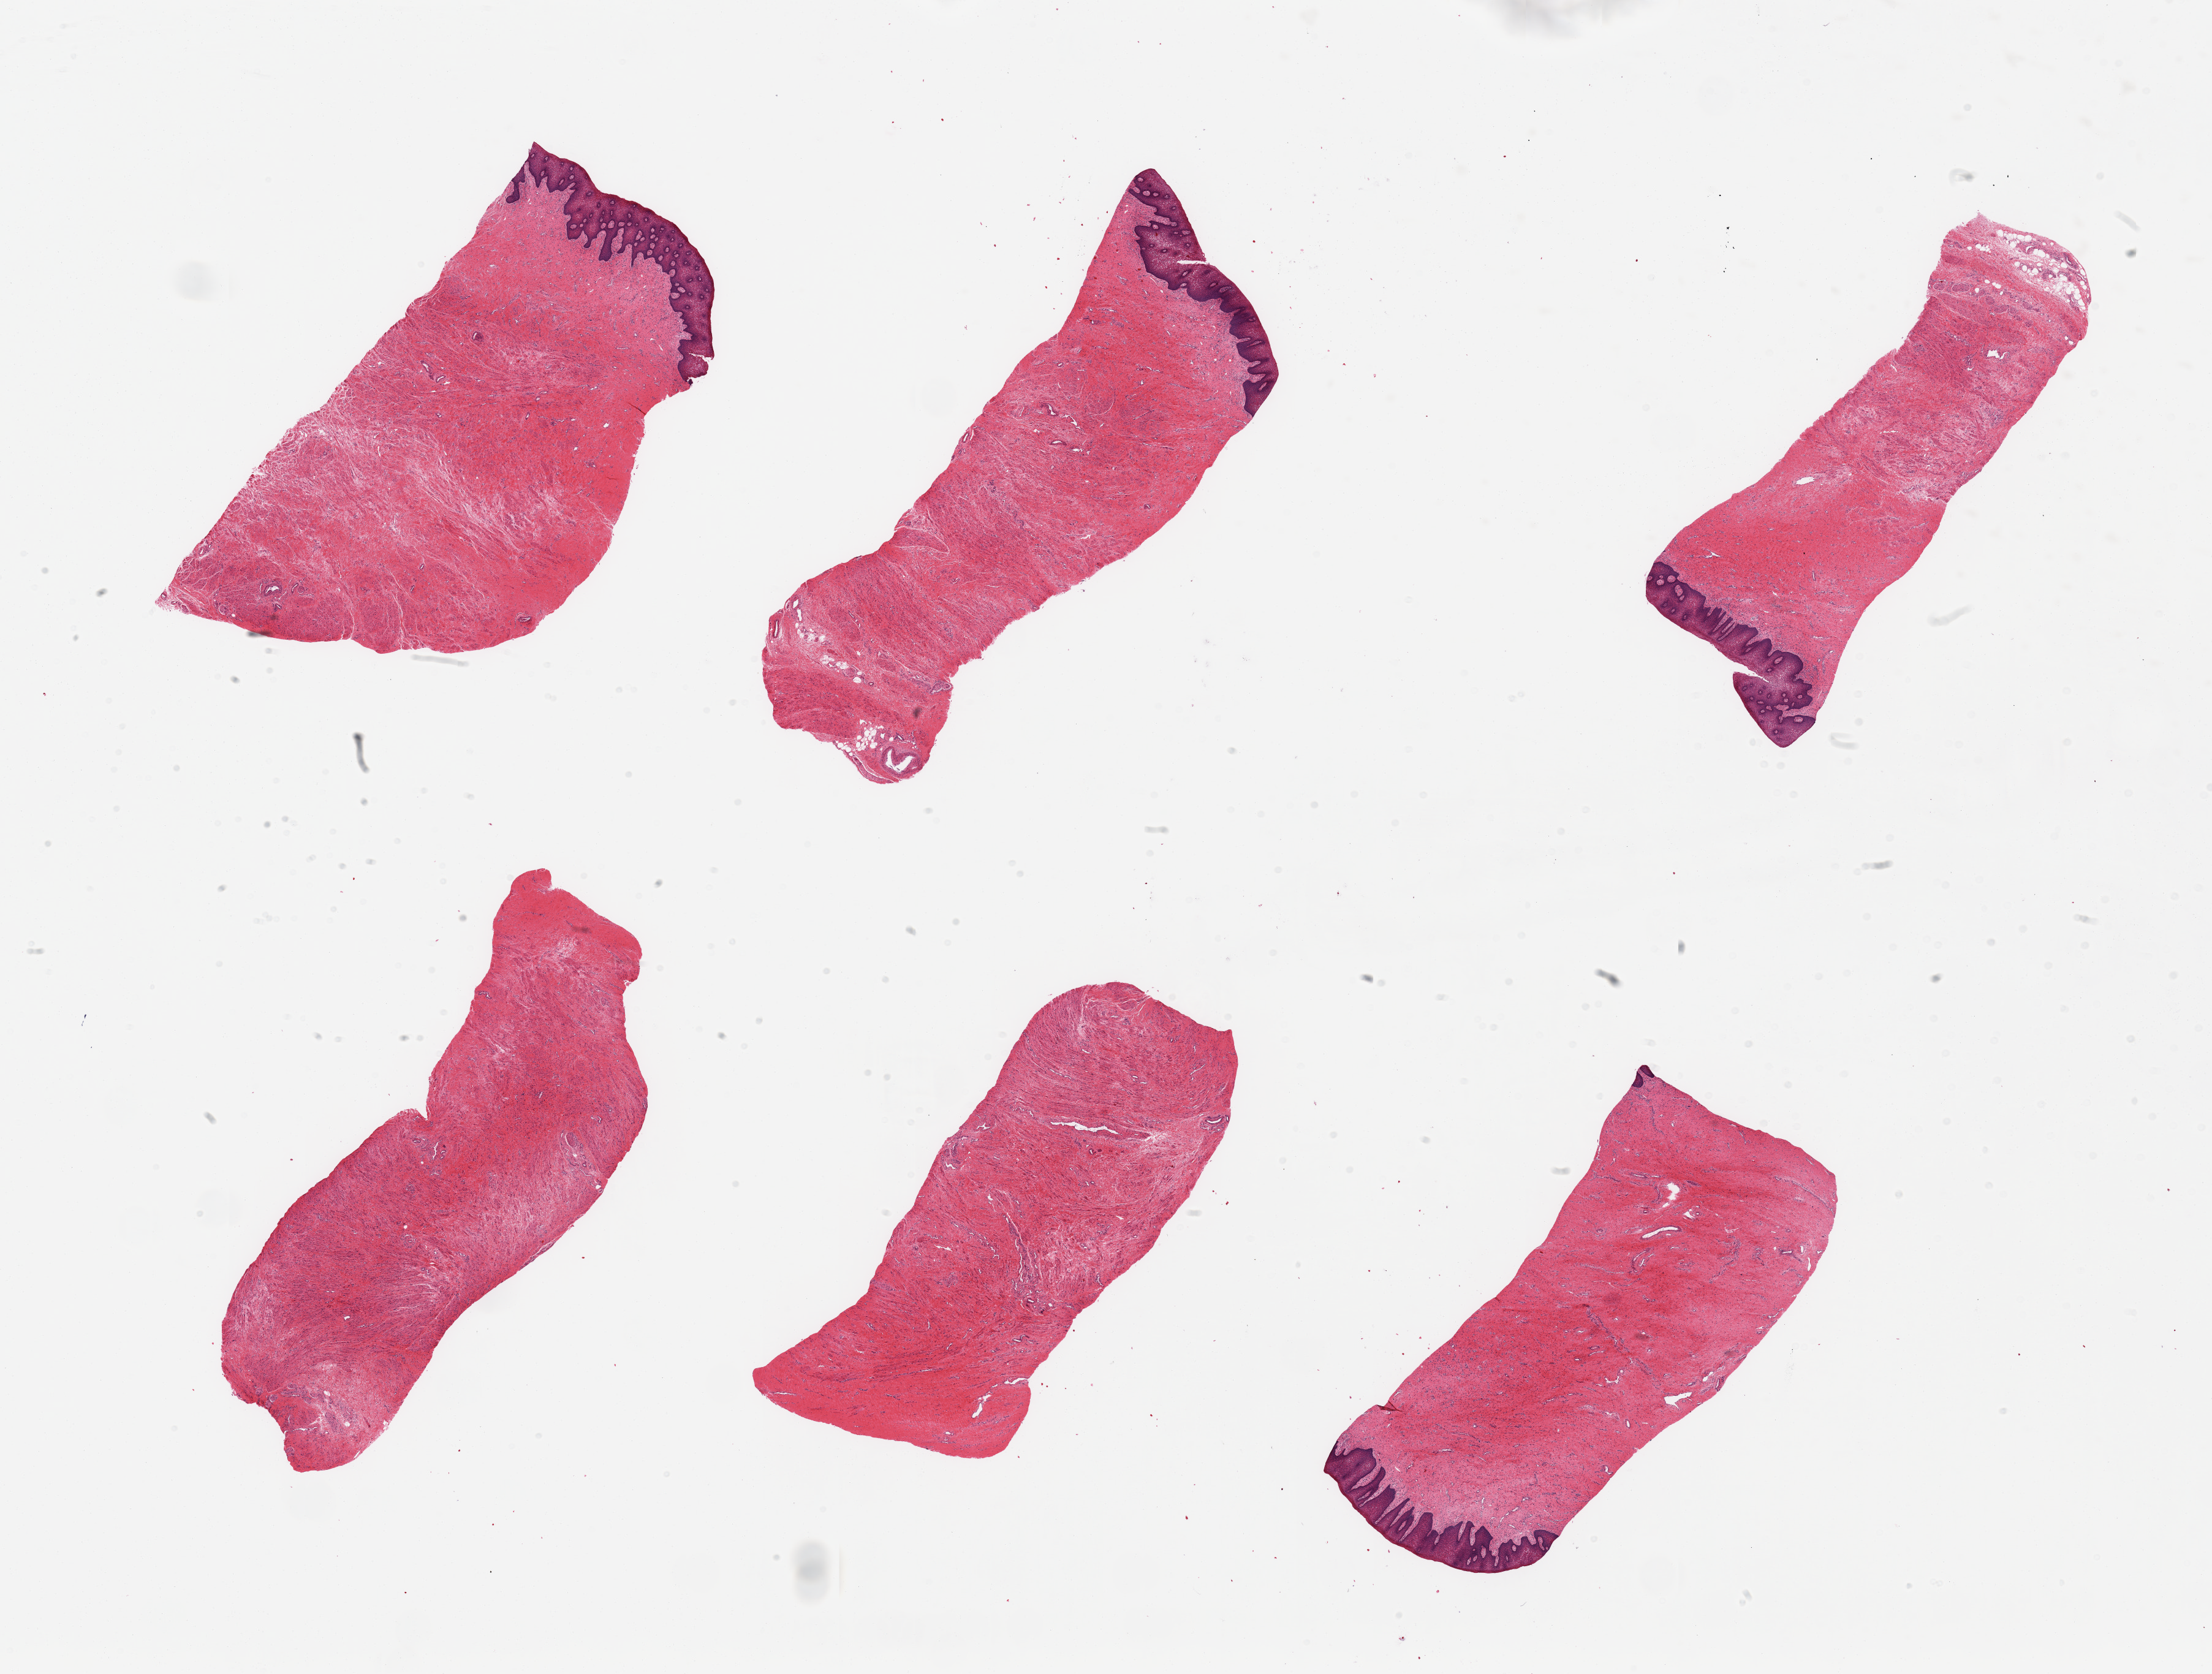
Whole-slide image, haematoxylin and eosin stain, a low-resolution overview of the entire scanned area, about 28.5 x 21.6 mm (from a 20x scan), PAXgene-fixed paraffin-embedded (PFPE) section, section of vagina (target tissue), donor tissue sample.
• reviewer comment on this tissue sample: 6 pieces, two lack epithelium